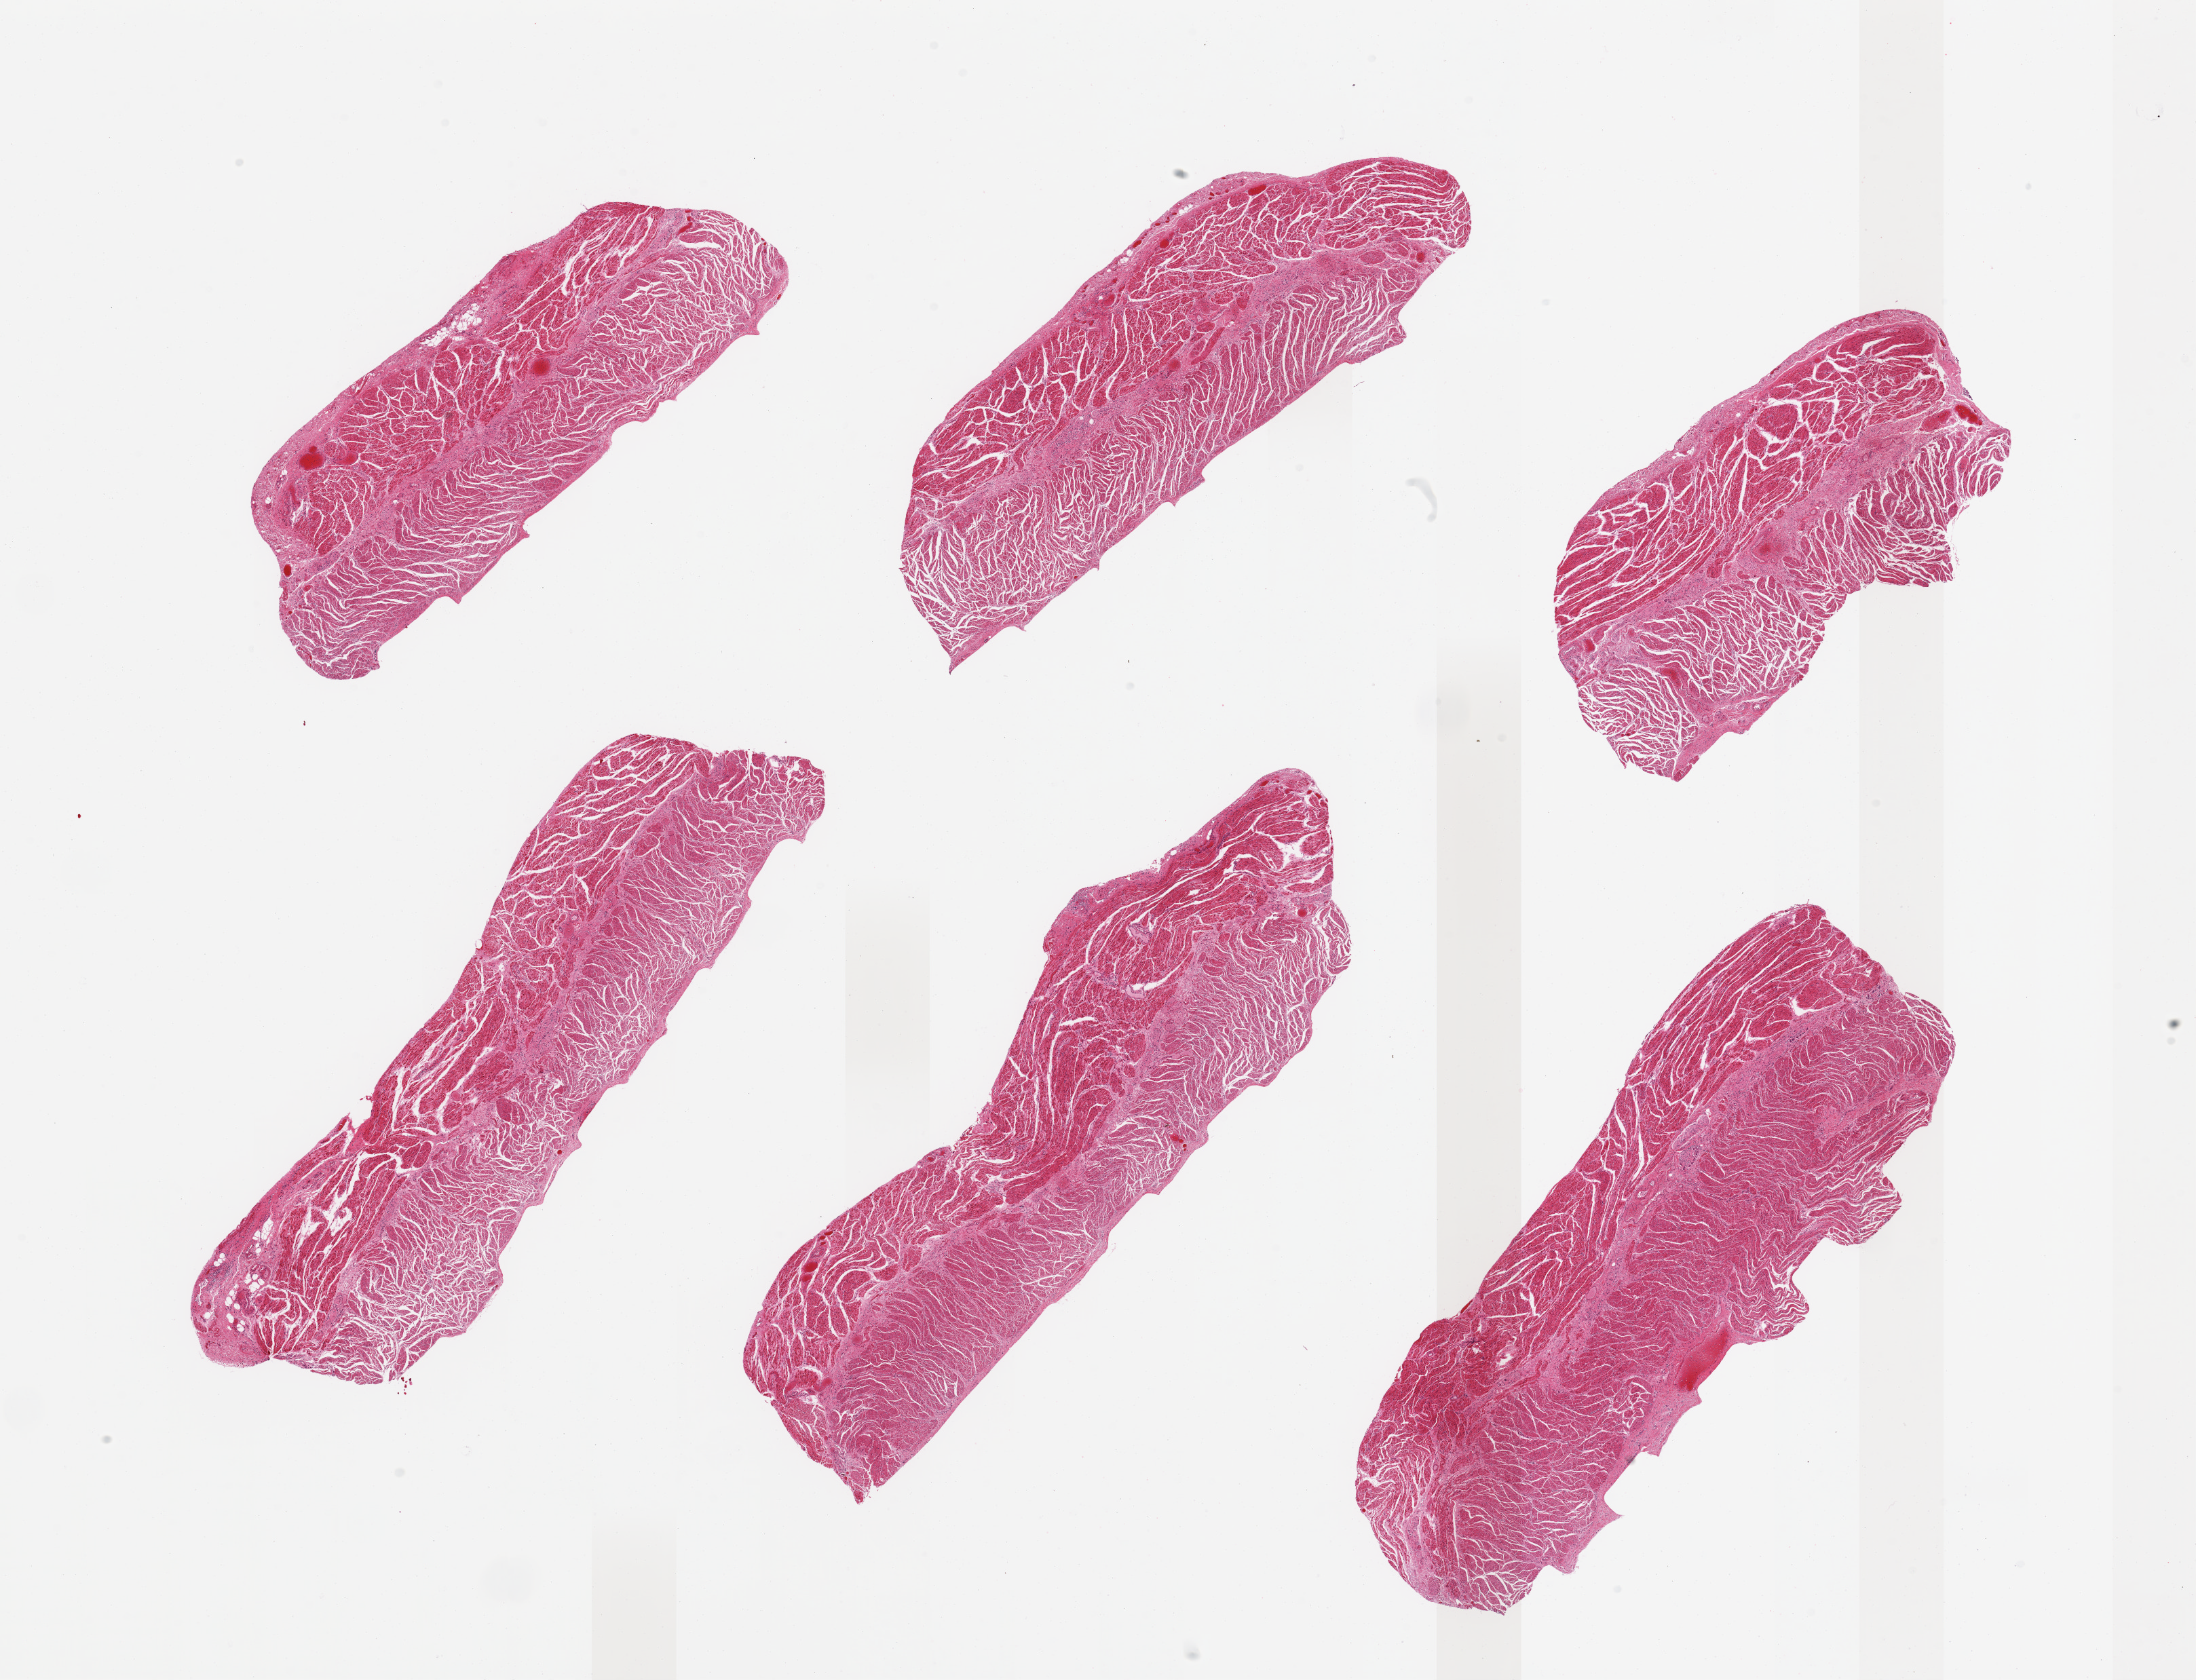
Digitized haematoxylin and eosin-stained section — whole scanned area (about 25.6 x 19.6 mm, from a 20x scan) shown as a low-resolution overview. PAXgene-fixed, paraffin-embedded tissue. Target tissue: gastroesophageal junction. Donor tissue sample. Female donor.
- review note (as recorded): 6 pieces, confirmed target muscularis